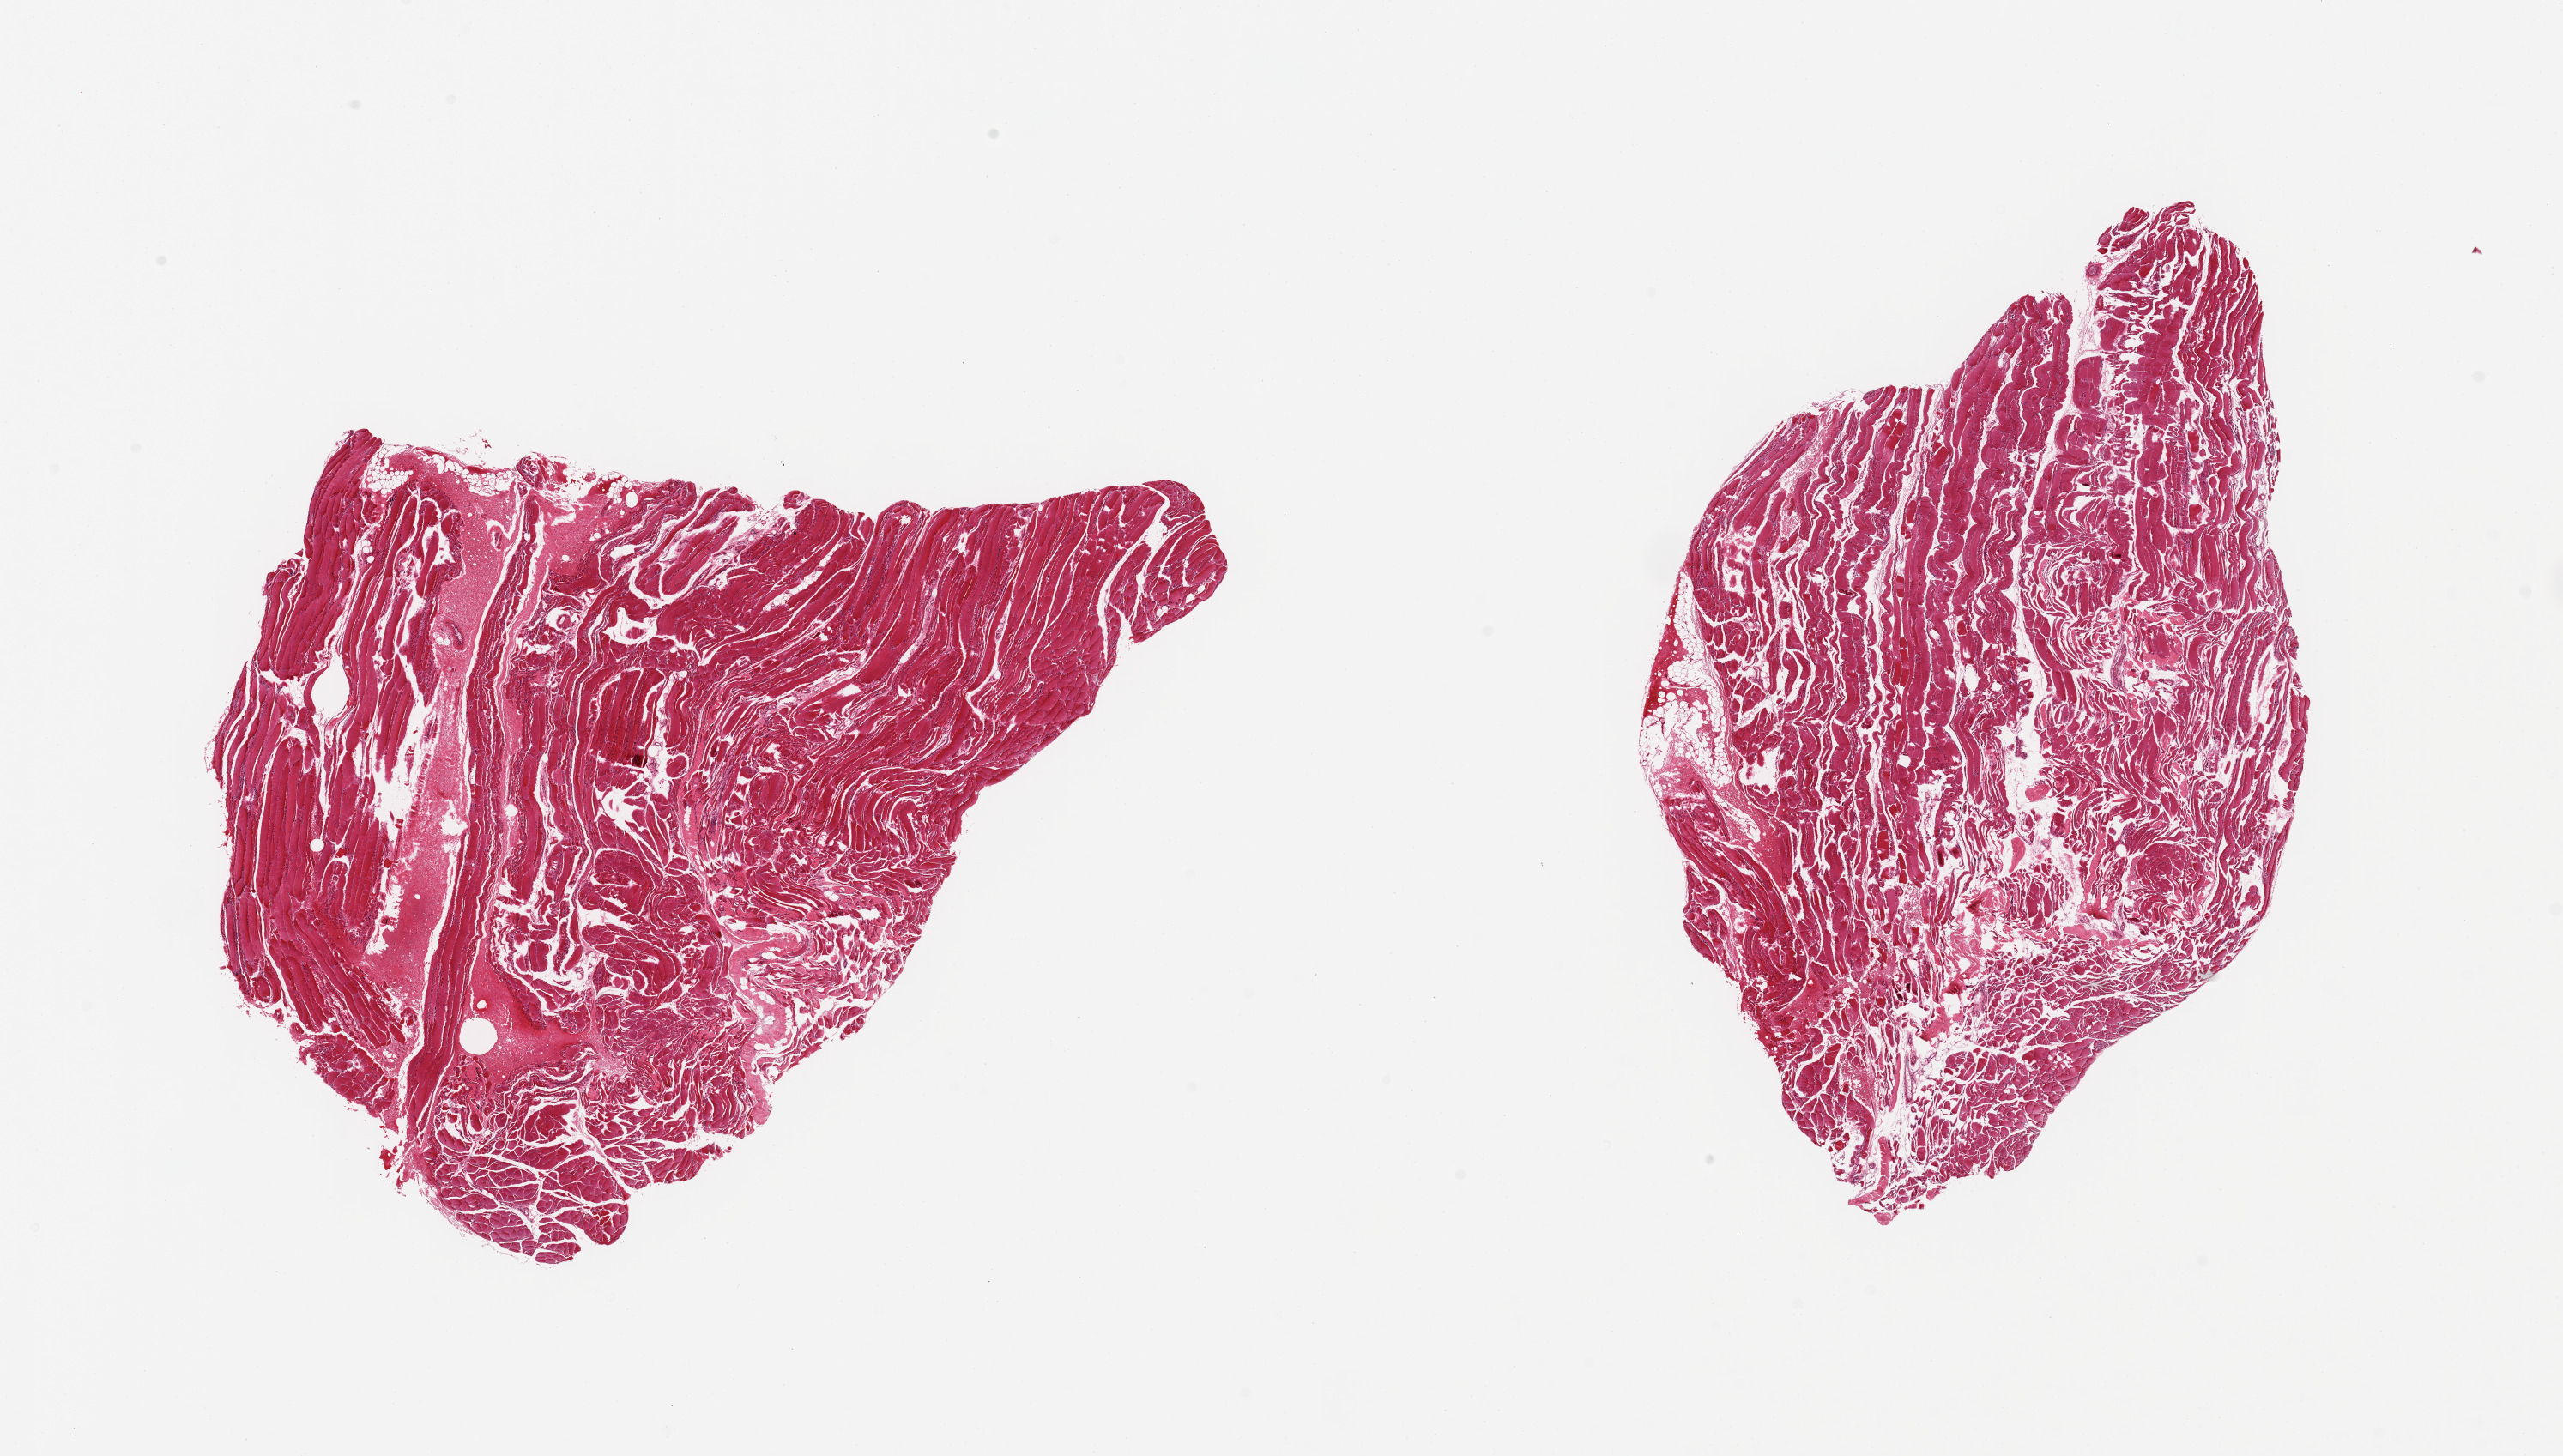
Digitized H&E-stained section — a low-resolution overview of the entire scanned area, about 23.6 x 13.4 mm; PAXgene-fixed, paraffin-embedded tissue; section of skeletal muscle (target tissue); donor tissue sample. Male donor.
Review note (as recorded): 2 pieces; patchy atrophy.